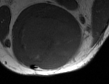
MRI of an extremity soft-tissue mass, one axial slice; position 31 of 50 along the scan axis; MR volume resampled by the dataset authors to the PET/CT grid (not the native acquisition matrix); 3.27 mm slice thickness; 109 × 84 image matrix, field of view 106 × 82 mm. Male patient. From the clinical record (not read from this slice): histological type: synovial sarcoma; site of the primary tumour: left poplietal fossa.
Annotated regions visible in this slice (expert contour drawn on MRI and transferred to this co-registered scan by the dataset authors):
- gross tumour volume (mass): bounding box [x1, y1, x2, y2] px = [16, 16, 83, 68]